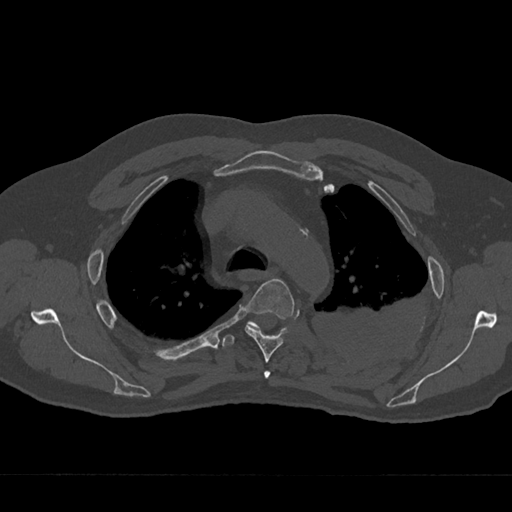
CT including the spine, one axial slice. Reconstruction kernel Br40s/3. Bone window (W 1800 / L 400 HU). 0.5 mm slice thickness. 512 × 512 image matrix. Patient: male, 75 years. From the clinical record (not read from this slice): primary cancer: renal; vertebrae with lytic lesions (as recorded): T4.
Annotated regions visible in this slice (semi-automatically segmented with operator editing):
- T3 vertebra: bounding box [x1, y1, x2, y2] px = [264, 371, 271, 378]
- T4 vertebra: [245, 278, 294, 363]
- T5 vertebra: [222, 321, 285, 348]